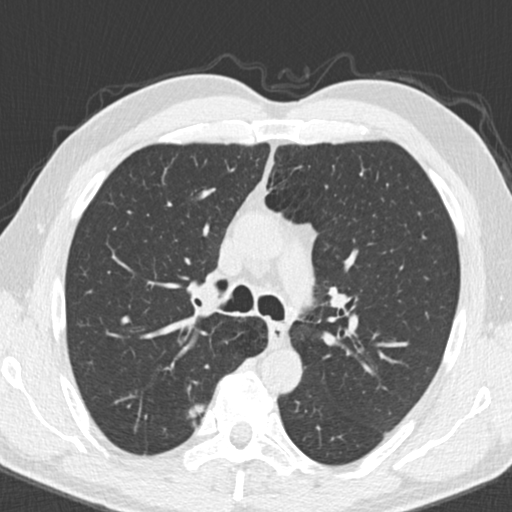
Low-dose screening chest CT, one axial slice; 120 kVp; lung window (W 1500 / L -600 HU); 2 mm slice thickness; 512 × 512 image matrix, field of view 307 × 307 mm.
Outlined on this slice (expert manual segmentation):
- lesion 1 (tumor, upper lobe of right lung): bounding box (x1, y1, x2, y2) in pixels: (187, 404, 206, 428)